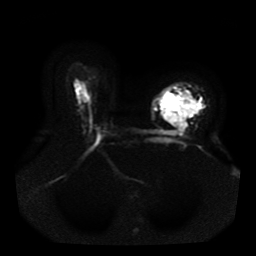
Breast MRI, one axial slice. Slice 28 of 41 in the series (ordered by position). Diffusion-weighted series; image 2 of 4 stored at this slice position (different b-values; order by instance number). 1.5 T. 5 mm slice thickness. 256 × 256 image matrix, field of view 330 × 330 mm. Female patient.
Annotated regions visible in this slice (manually delineated by an expert):
- tumour on diffusion-weighted imaging: bounding box [x1, y1, x2, y2] px = [160, 92, 200, 129]